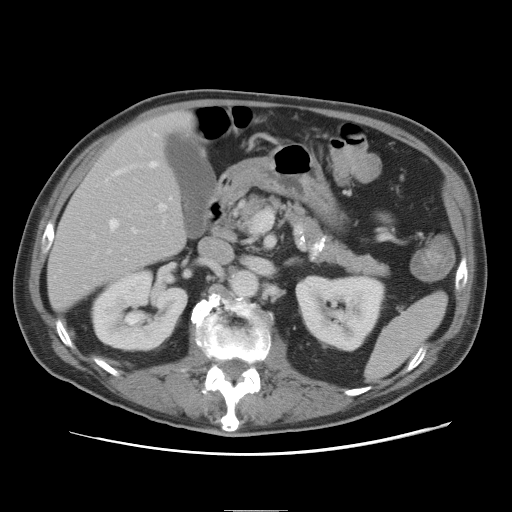
Contrast-enhanced abdominal CT, one axial slice; position 35 of 89 along the scan axis; 120 kVp; intravenous contrast given; soft-tissue window (W 400 / L 40 HU); 5 mm slice thickness; 512 × 512 image matrix, field of view 375 × 375 mm. Male patient, age 69 years. Case-level facts recorded for this patient, not image findings: diagnosis: colorectal cancer liver metastases, imaged before liver resection; multiple liver metastases: no; largest metastasis: 8.5 cm; disease in both lobes: no.
Annotated regions visible in this slice (outlined manually by an expert reader):
- hepatic veins: bounding box [x1, y1, x2, y2] px = [110, 134, 172, 232]
- liver: [48, 113, 192, 310]
- planned liver remnant (the part of the liver to remain after resection): [48, 114, 191, 311]
- portal vein (with intrahepatic branches): [109, 203, 167, 252]